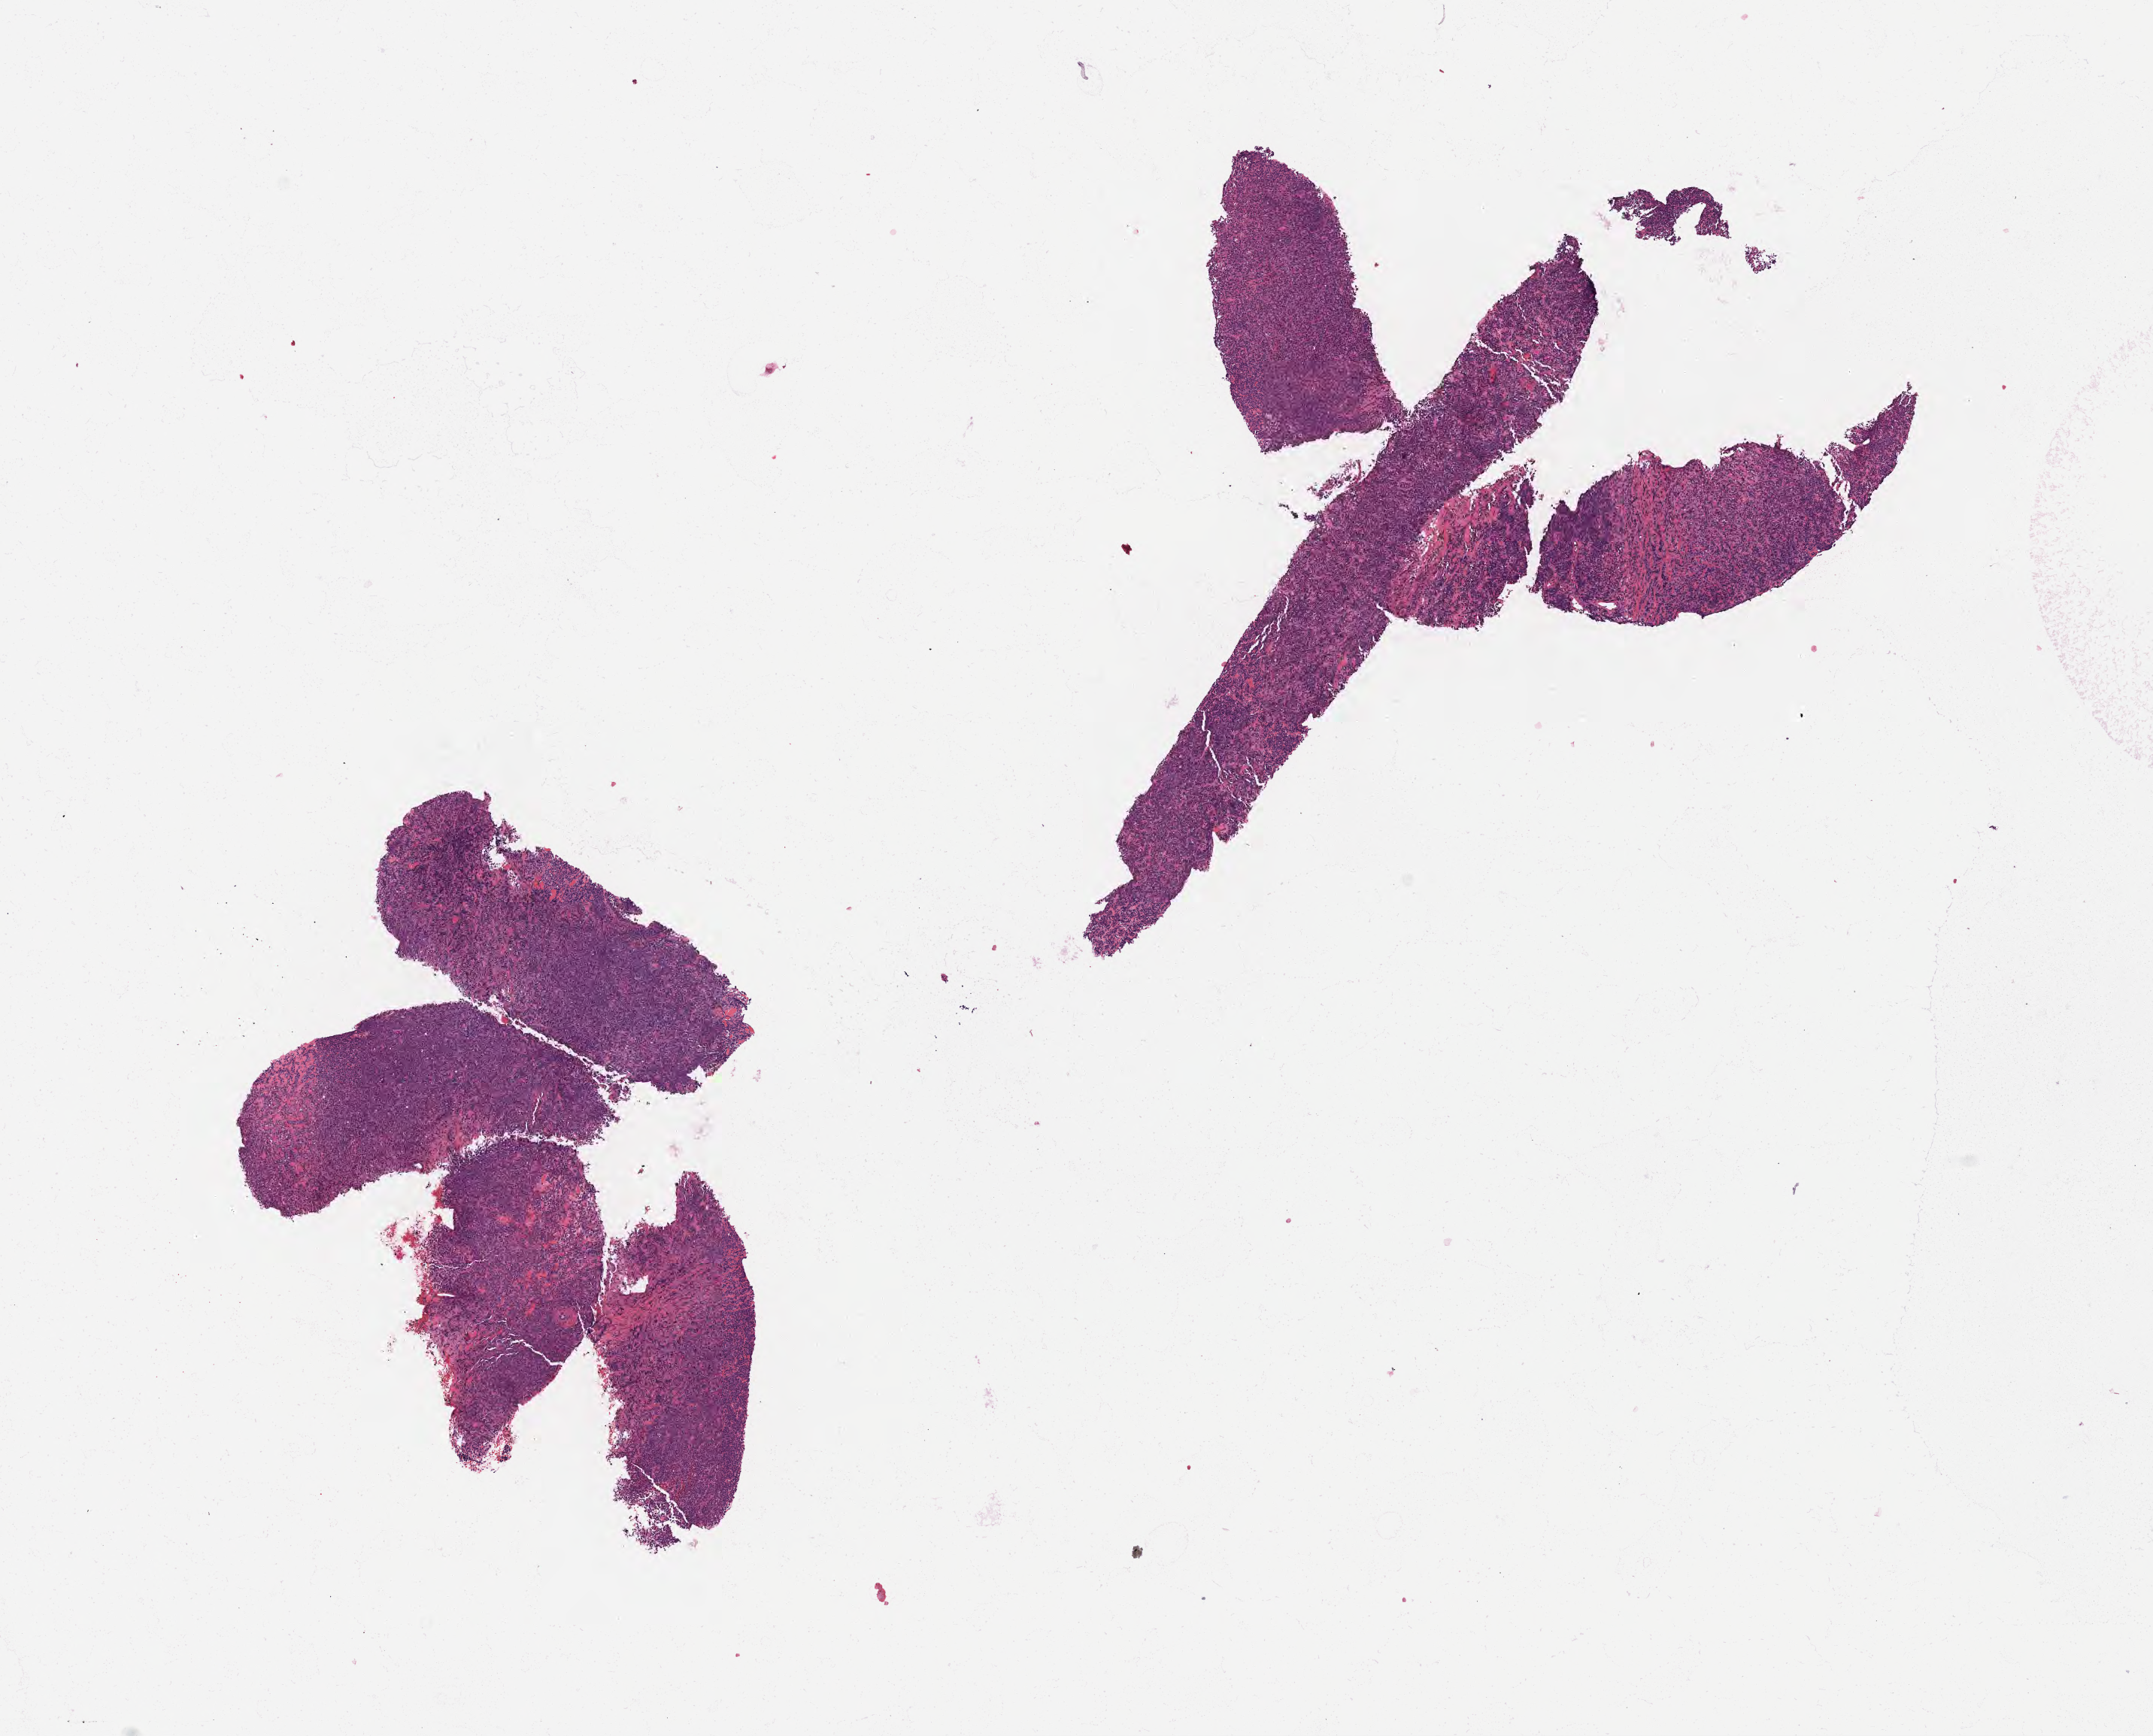
H&E whole-slide image — shown as a low-resolution overview of the whole scanned area (about 11.6 x 9.3 mm); specimen: tumor tissue; anatomic site: lymph node. Male patient, age 54 years.
• diagnosis: Diffuse large B-cell lymphoma, NOS